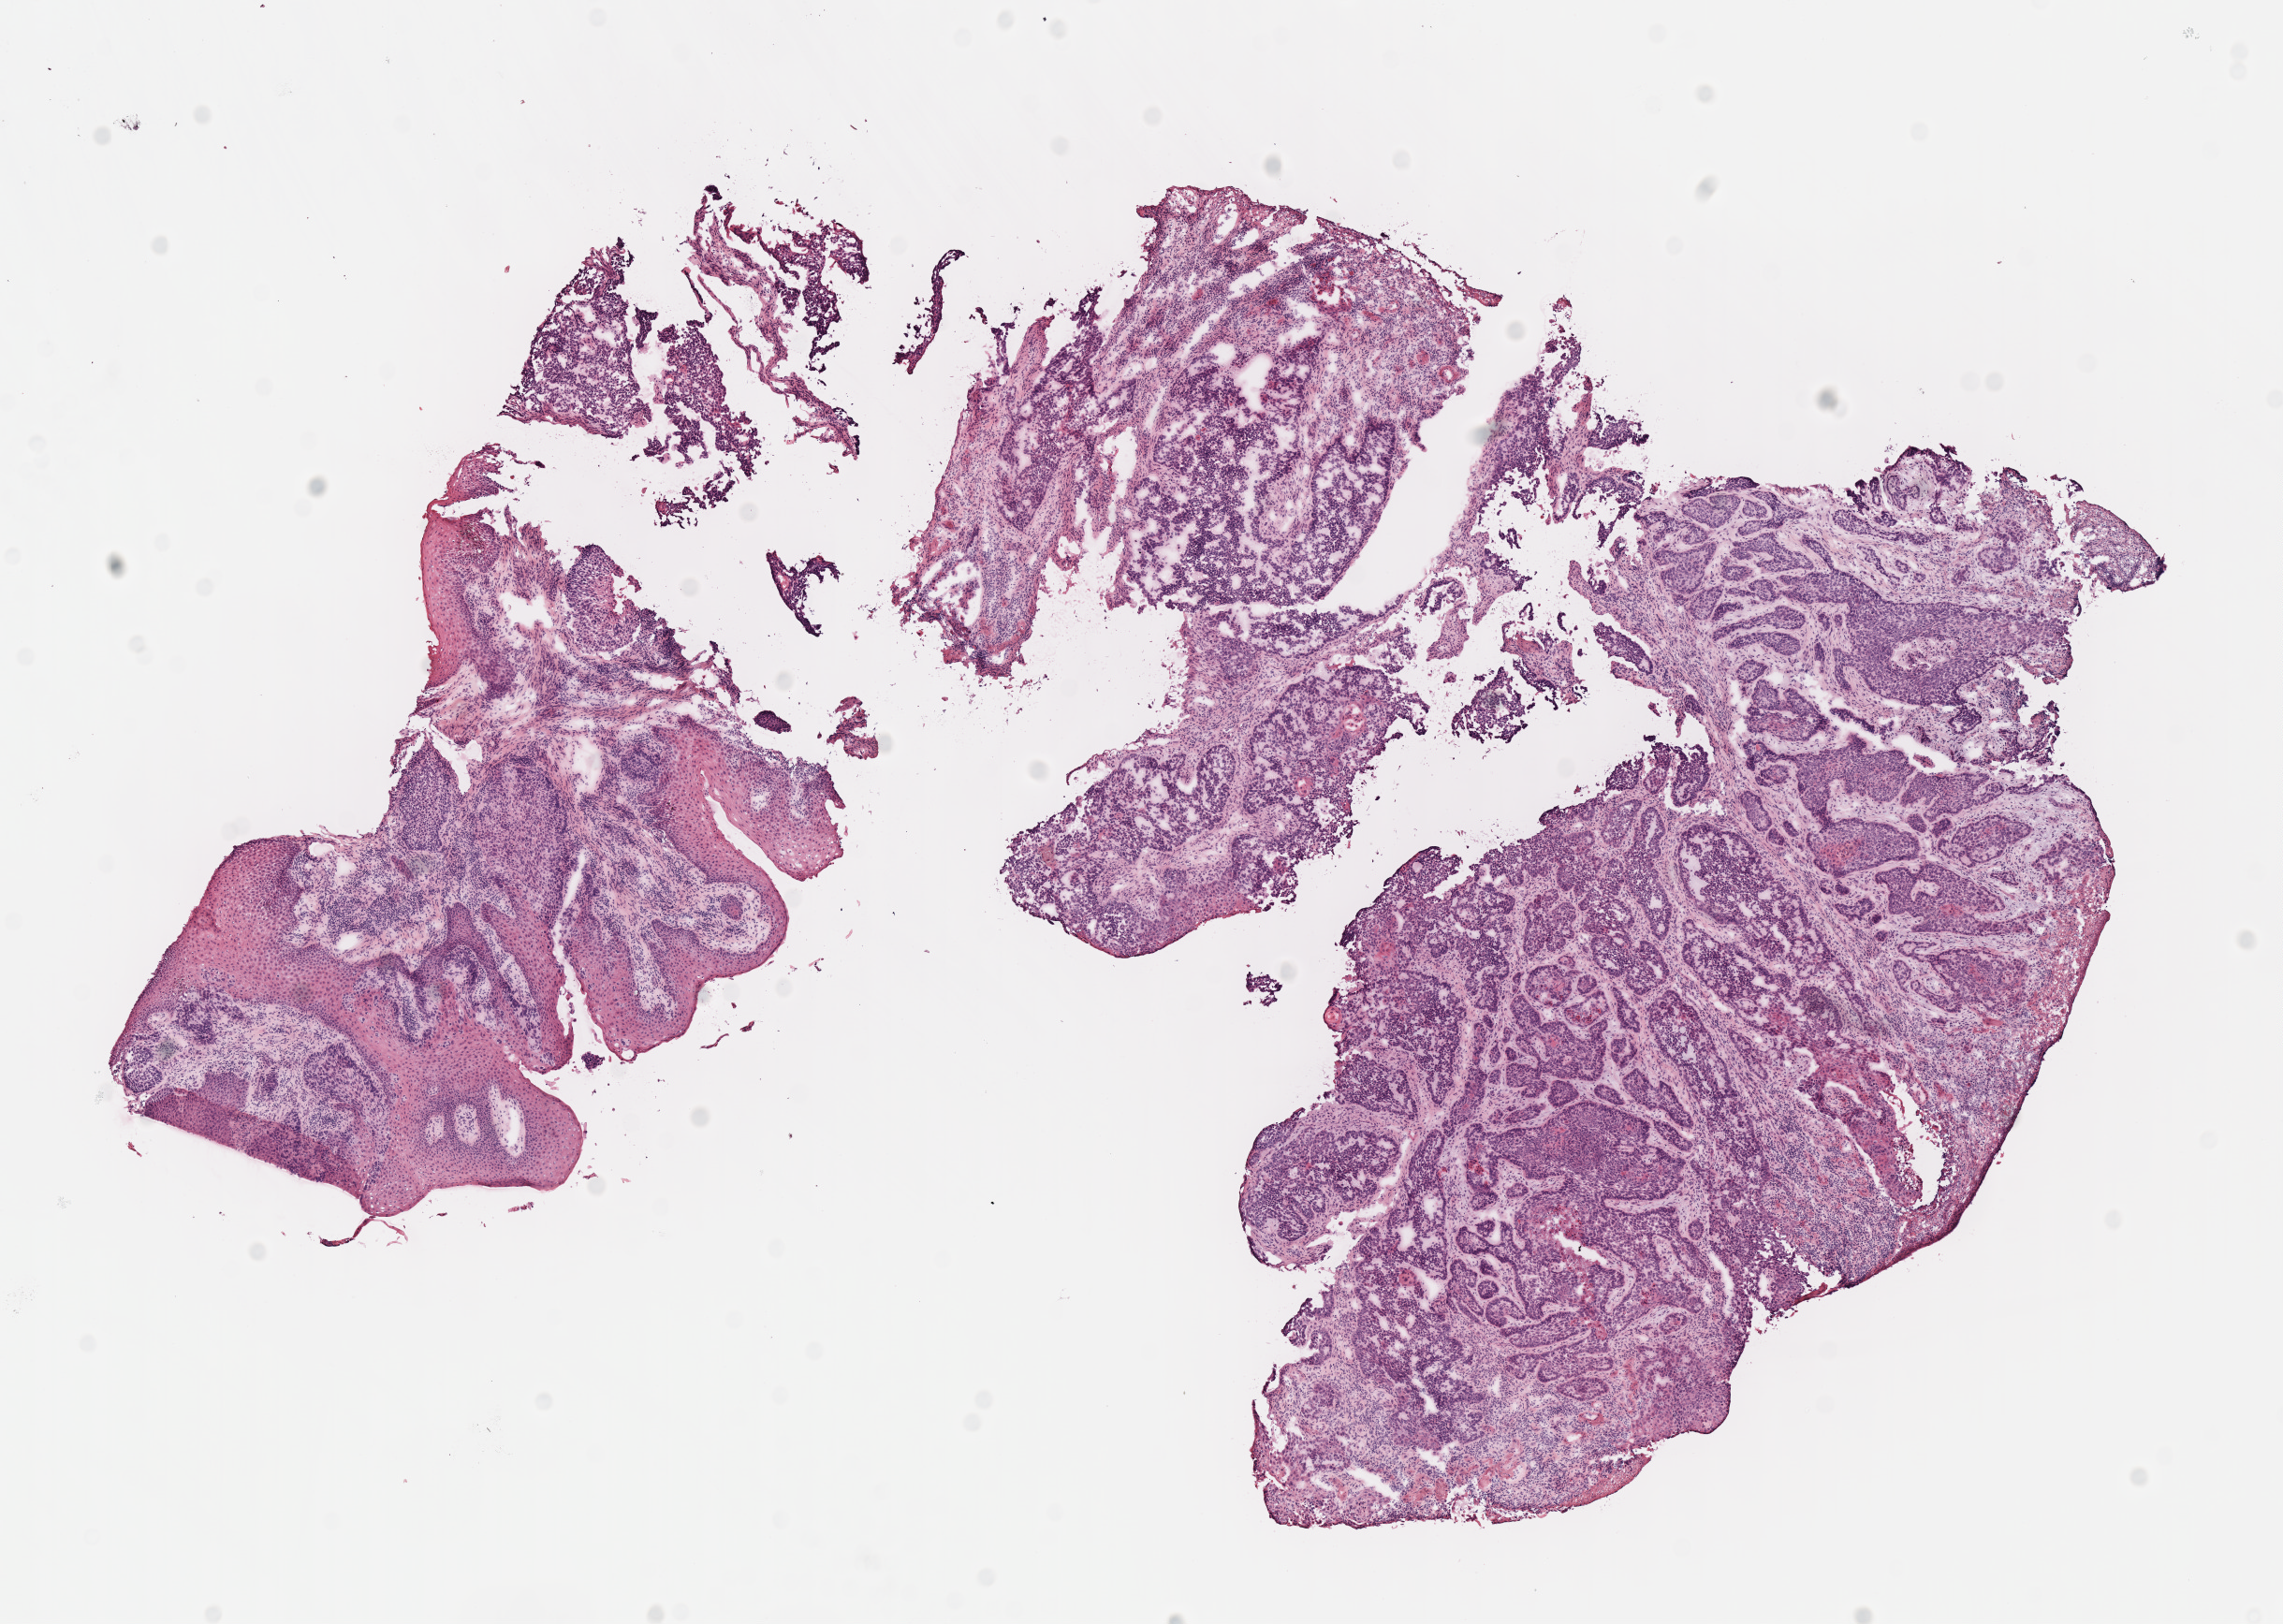
Hematoxylin and eosin (H&E) stained whole-slide image, whole scanned area (about 9.6 x 6.8 mm) shown as a low-resolution overview; frozen section; sample: primary tumour, head and neck. Patient: male, age at initial diagnosis 70 years. Histologic grade: G4 (undifferentiated). Slide review estimates, as recorded: tumour cells 80%, tumour nuclei 80%, normal cells 10%, stromal cells 9%, necrosis 1%. Infiltration values recorded for this section: lymphocyte infiltration 10%.
Histologic diagnosis: Squamous cell carcinoma, NOS (larynx, NOS).